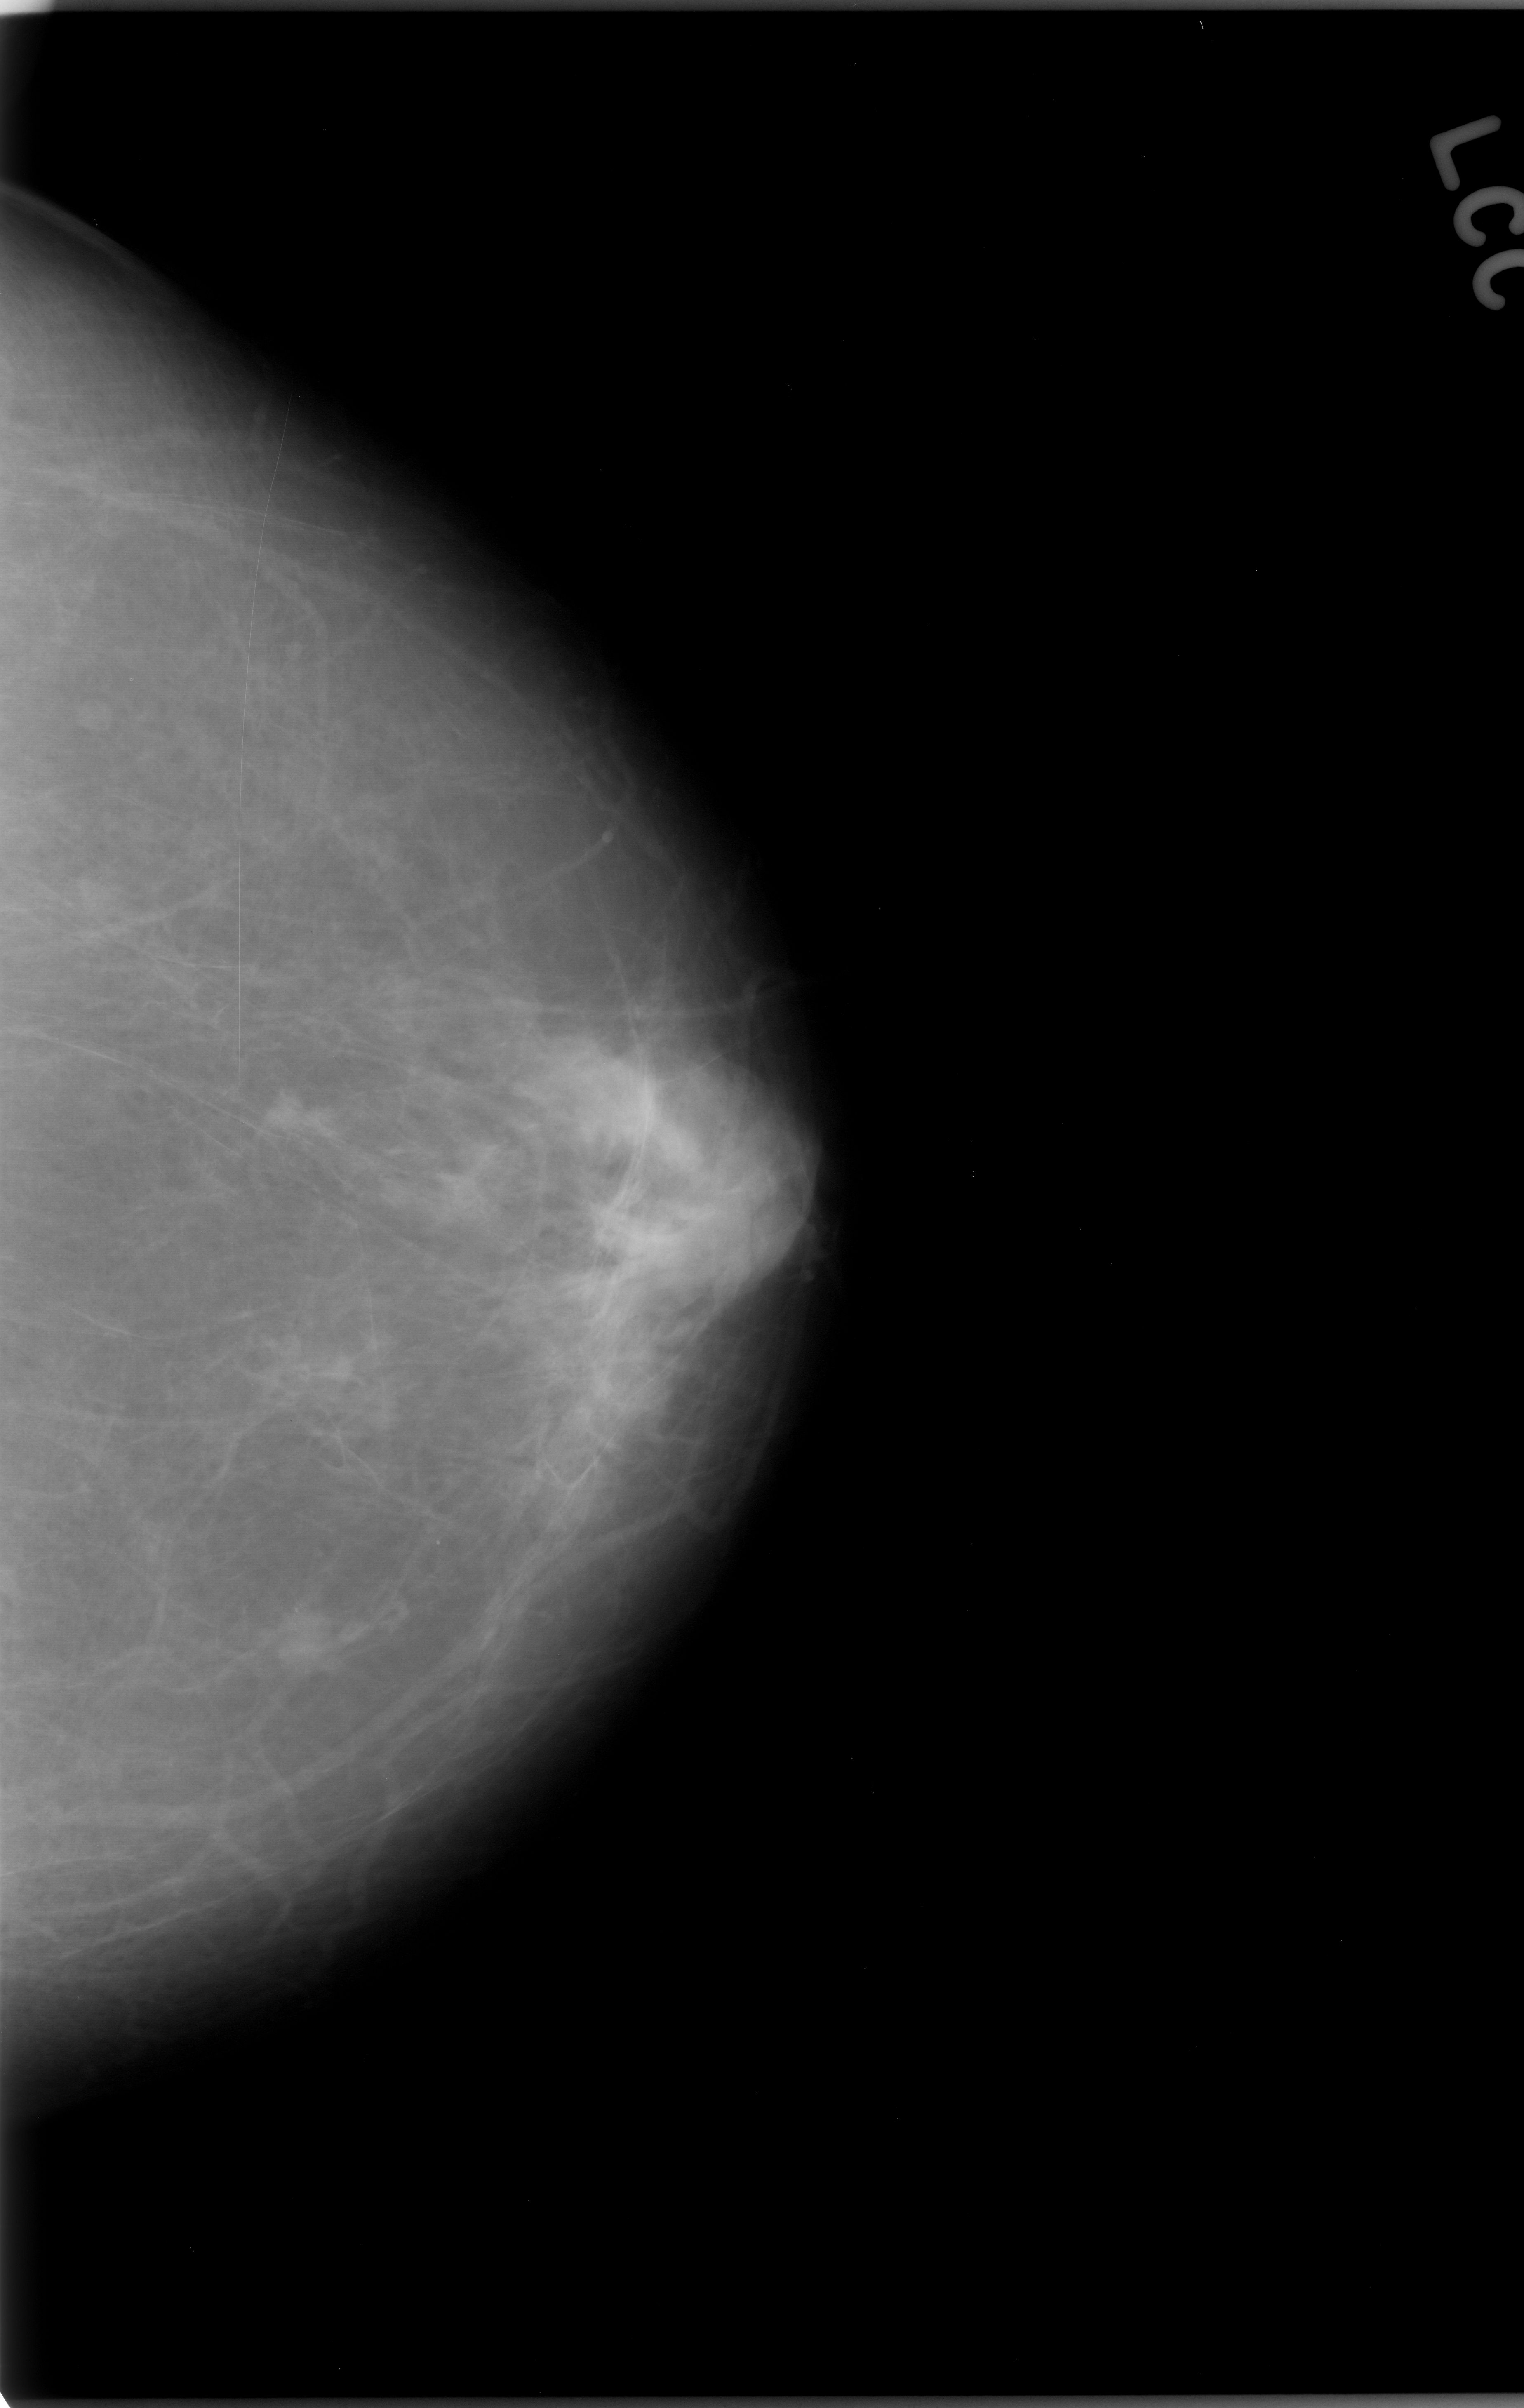
Scanned film-screen mammogram. Left breast. CC view. Breast composition: almost entirely fatty (BI-RADS density category 1 of 4). 1524 × 2408 image matrix.
Expert-marked regions of interest on this film, with their recorded descriptors:
- mass, shape lobulated, margins microlobulated; BI-RADS assessment category 5; subtlety rating 4 on a 1 (subtle) to 5 (obvious) scale; pathology (as recorded): malignant: bounding box [x1, y1, x2, y2] px = [237, 1582, 353, 1686]